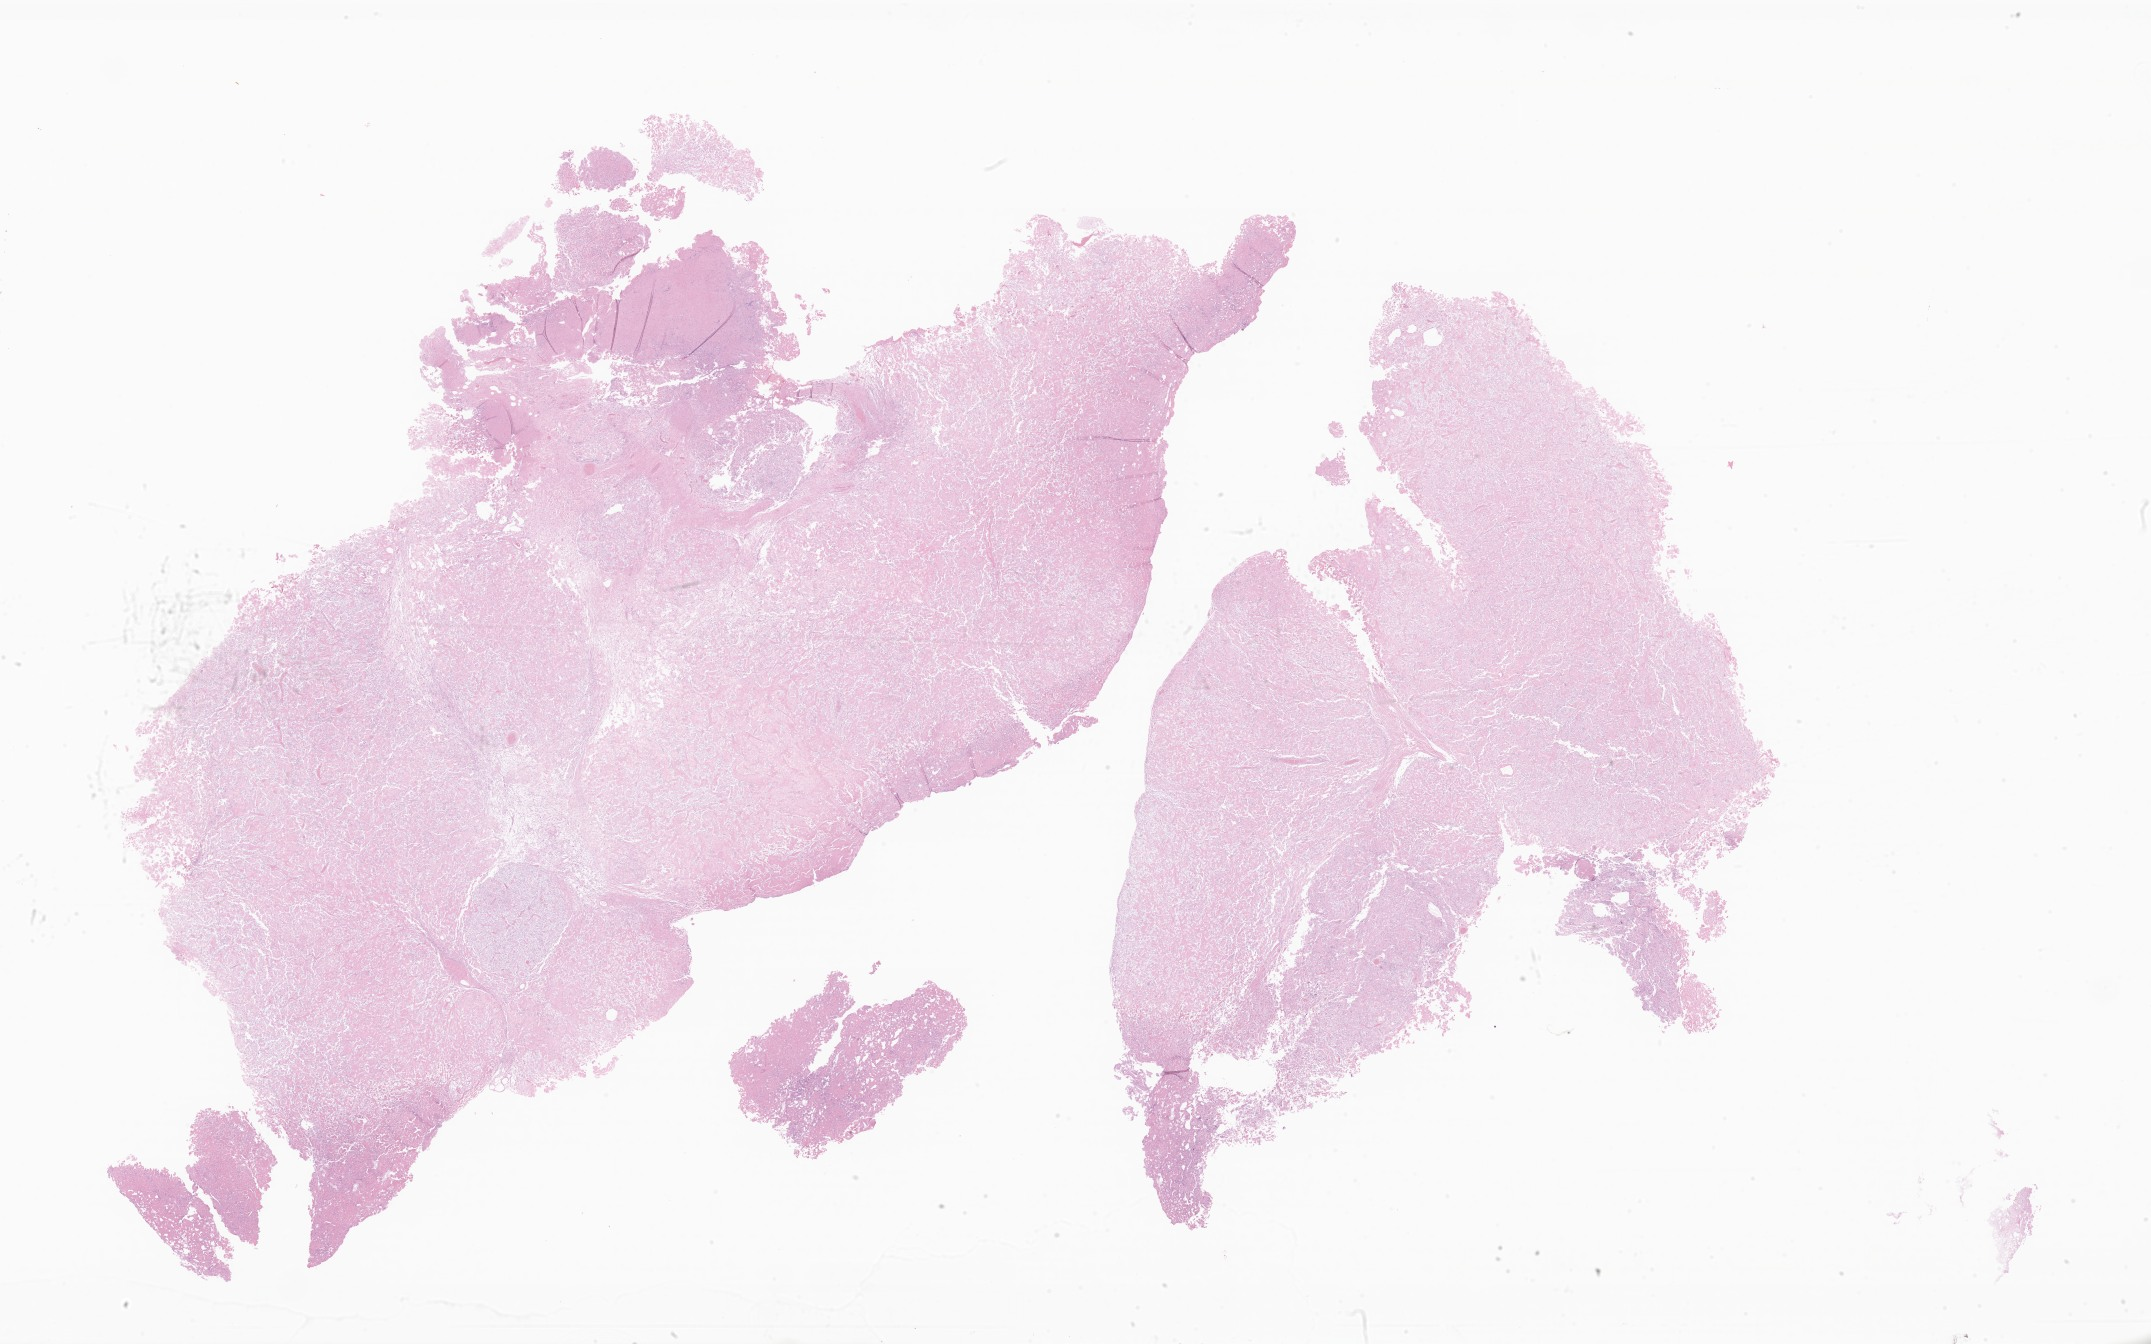
Digitized hematoxylin and eosin (H&E)-stained section of tumor tissue from the brain, shown as a low-resolution overview of the whole scanned area (about 36.3 x 22.7 mm). Formalin-fixed, paraffin-embedded (FFPE) tissue. Male patient, age 243 months (20 years 3 months).
Diagnosis: Clear cell meningioma.